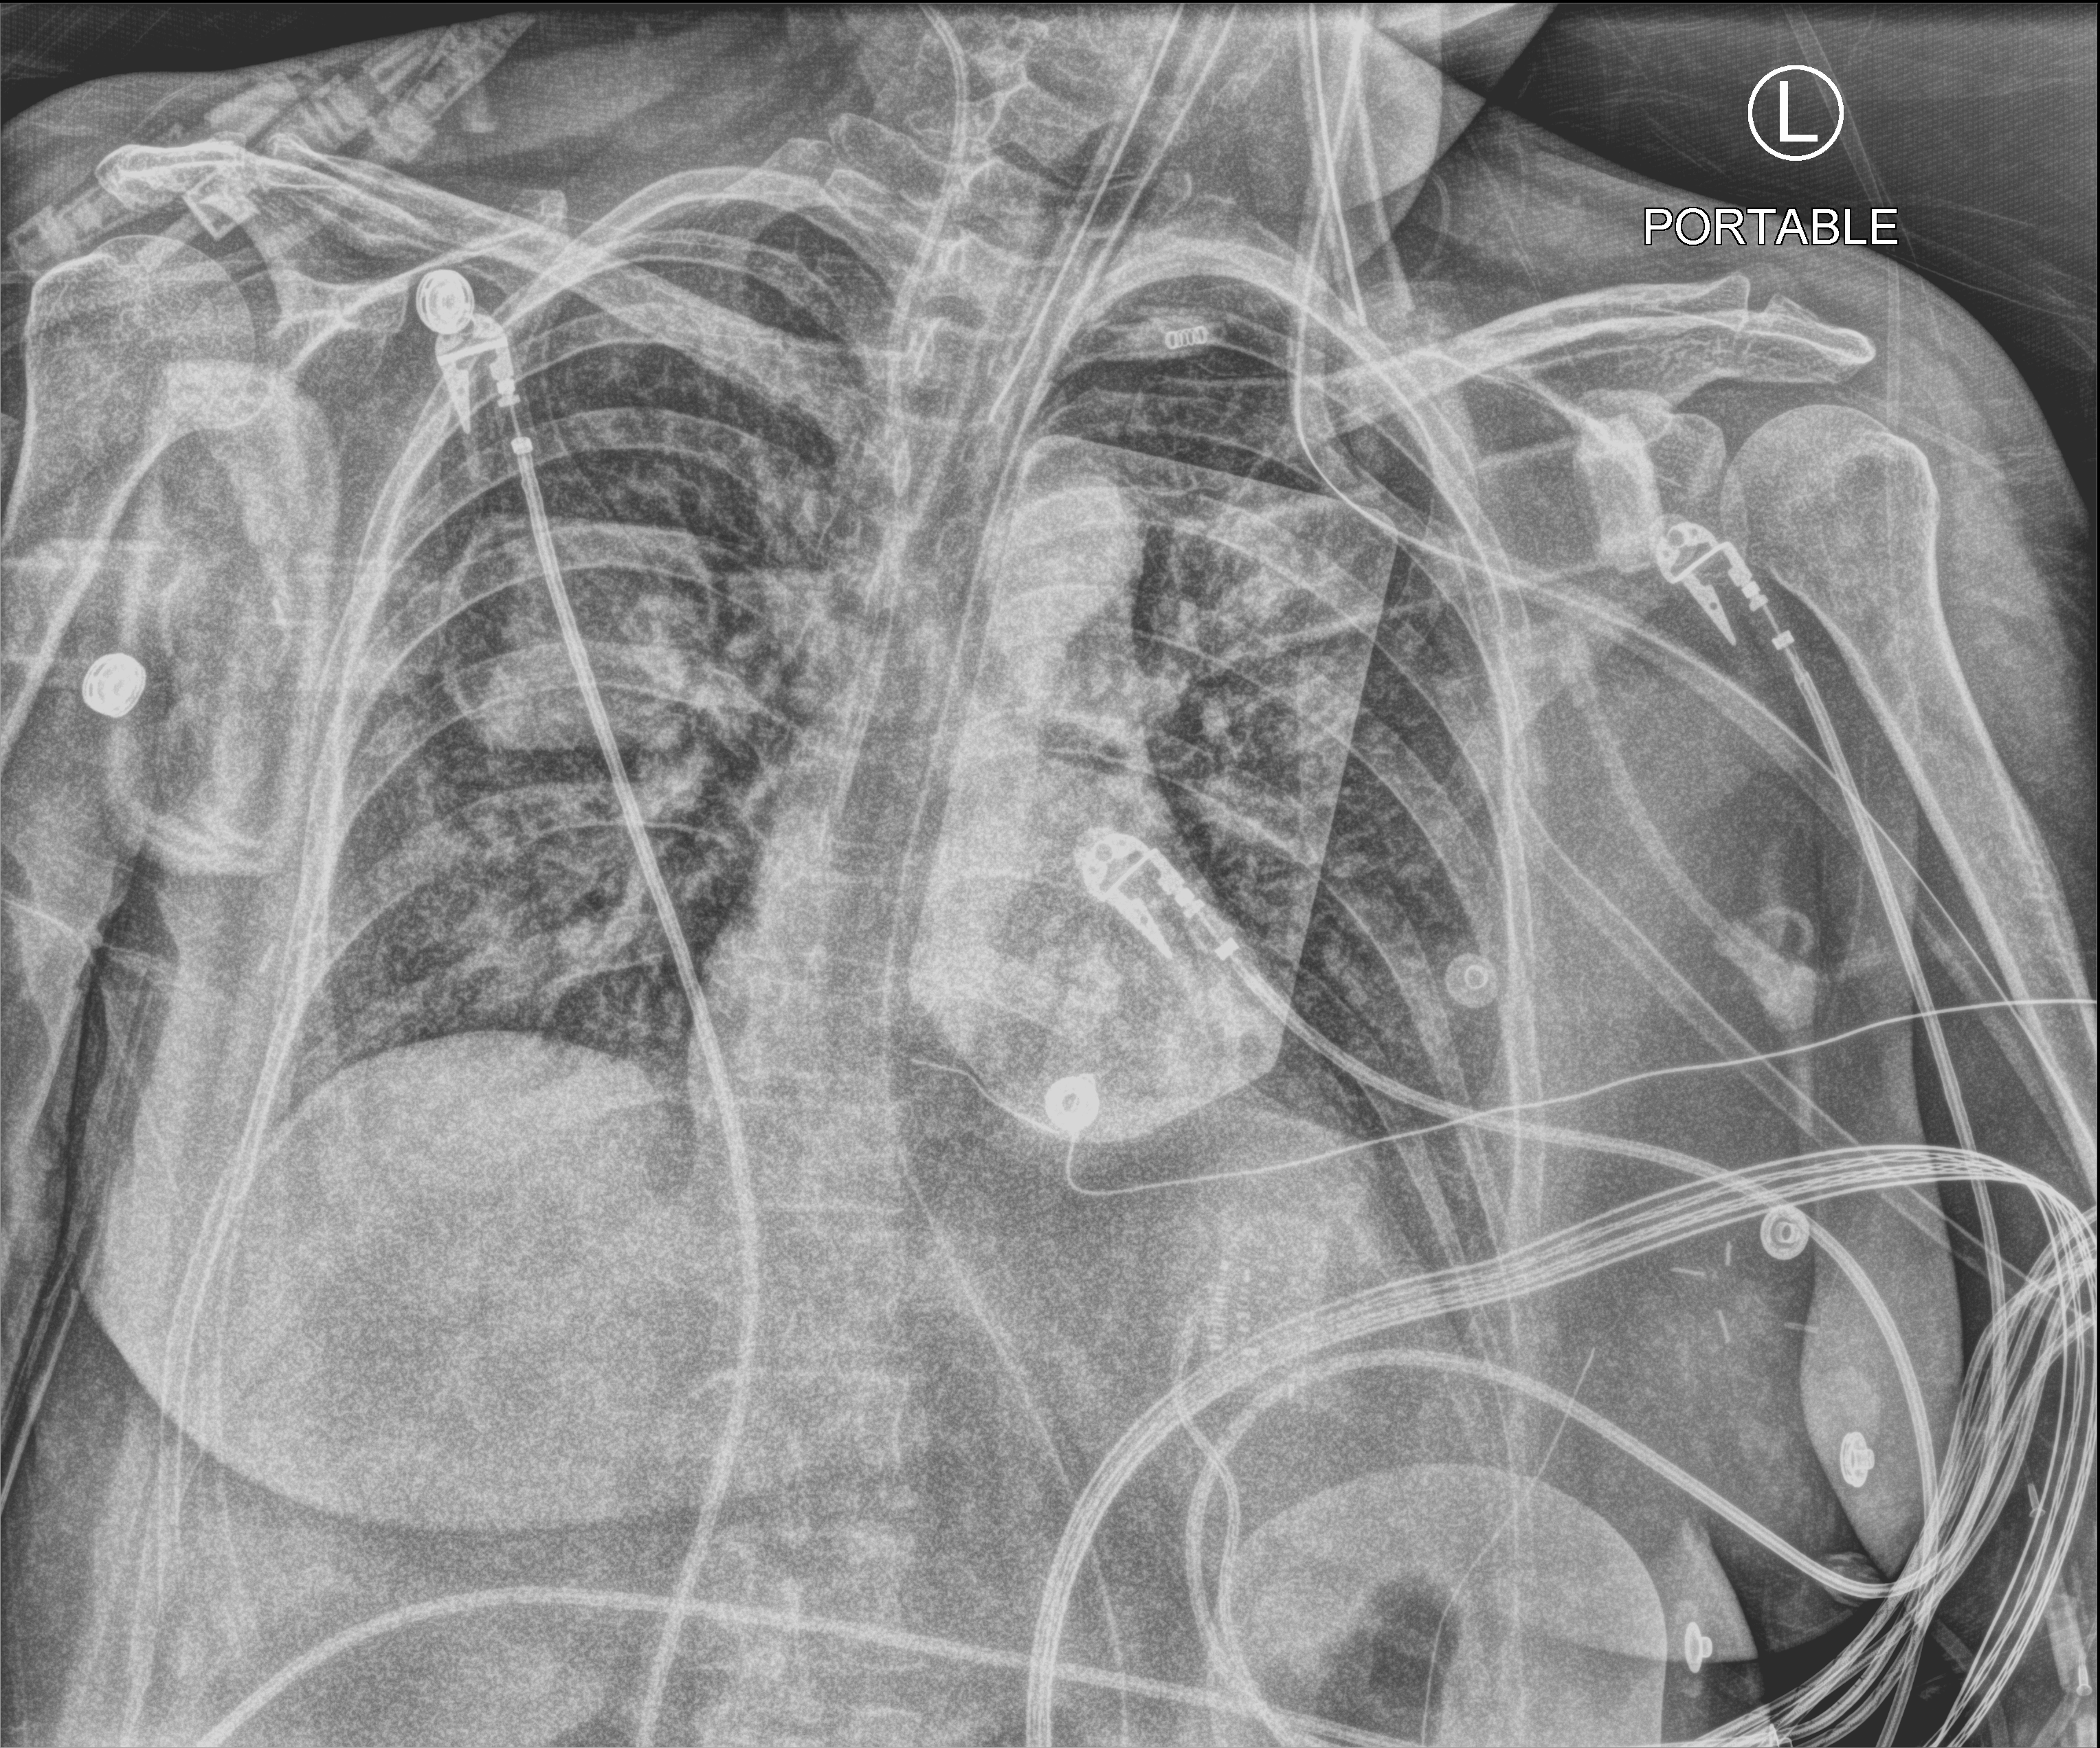
Chest X-ray (portable); anteroposterior (AP) projection. Female patient hospitalised with COVID-19, age 18–59 years.
Admission-level facts for this patient (not findings on this image; timing relative to this image not recorded): smoking status (admission record): never; admitted to intensive care during this hospital stay: no.